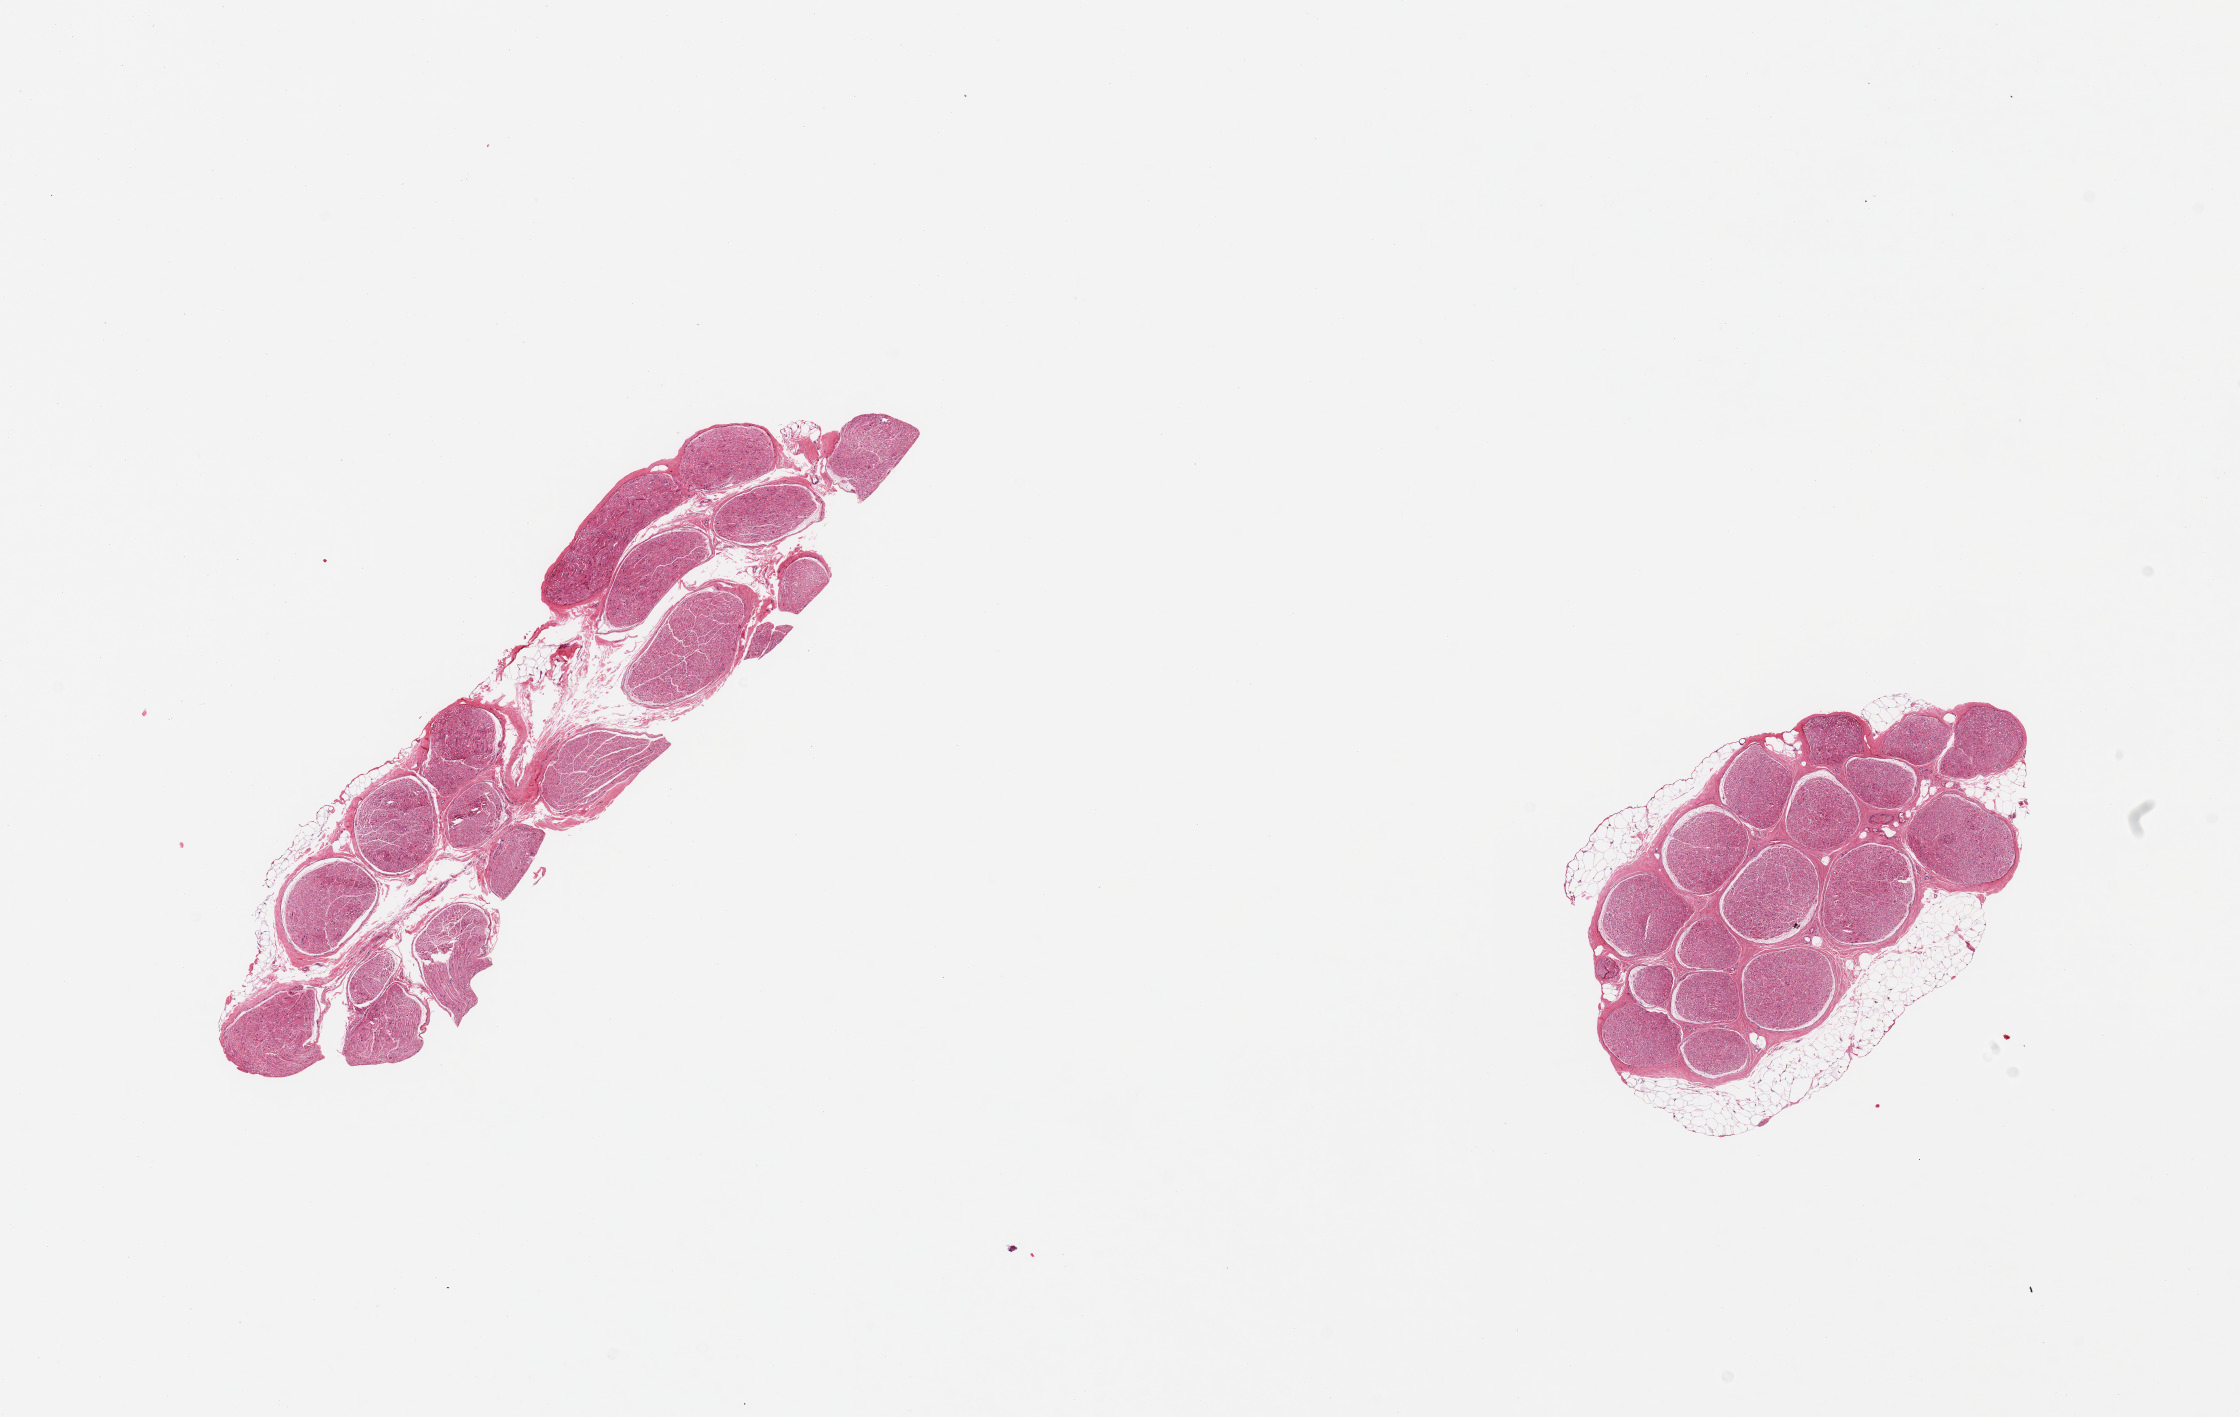
Haematoxylin and eosin whole-slide image, shown as a low-resolution overview of the whole scanned area (about 17.7 x 11.2 mm). PAXgene-fixed, paraffin-embedded tissue. Section of tibial nerve (target tissue). Donor tissue sample. Donor: female.
• pathologist's review note for this sample: 2 pieces; 30% internal fat on 1, 30% external fat on the other